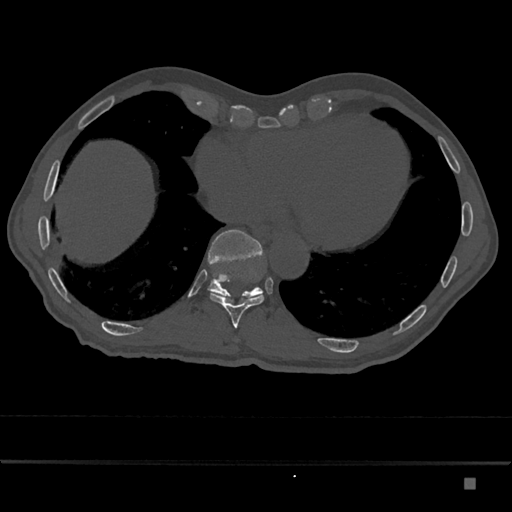
CT including the spine, one axial slice. Position 721 of 797 along the scan axis. Reconstruction kernel Br40s/3. Bone window (W 1800 / L 400 HU). 0.5 mm slice thickness. 512 × 512 image matrix. Male patient, age 72 years. From the clinical record (not read from this slice): primary cancer: prostate.
Annotated regions visible in this slice (semi-automatically segmented with operator editing):
- T10 vertebra: box from (x=210, y=293) to (x=264, y=328) px
- T11 vertebra: (x=208, y=230)–(x=263, y=302)